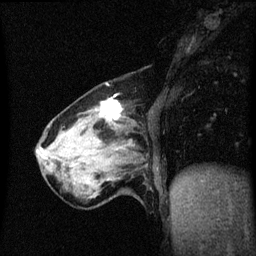
Breast MRI (dynamic contrast-enhanced), one sagittal slice. Position 18 of 60 along the scan axis. Dynamic contrast-enhanced series, image 2 of 3 at this slice position (ordered by acquisition). 1.5 T. TE 4.2 ms, TR 8.4 ms. 256 × 256 image matrix. Patient: female, 64 years. From the clinical record (not read from this slice): setting: breast cancer imaged before/during neoadjuvant chemotherapy; receptor status: HR-positive, HER2-negative.
Outlined on this slice (semi-automatically segmented with operator editing):
- analysis volume of interest (the breast-tissue region the enhancement analysis was run in; not a lesion): bounding box (x1, y1, x2, y2) in pixels: (56, 100, 137, 175)
- tumour enhancement mask (voxels above the 70 % enhancement threshold inside the analysis volume of interest): (102, 100, 123, 121)